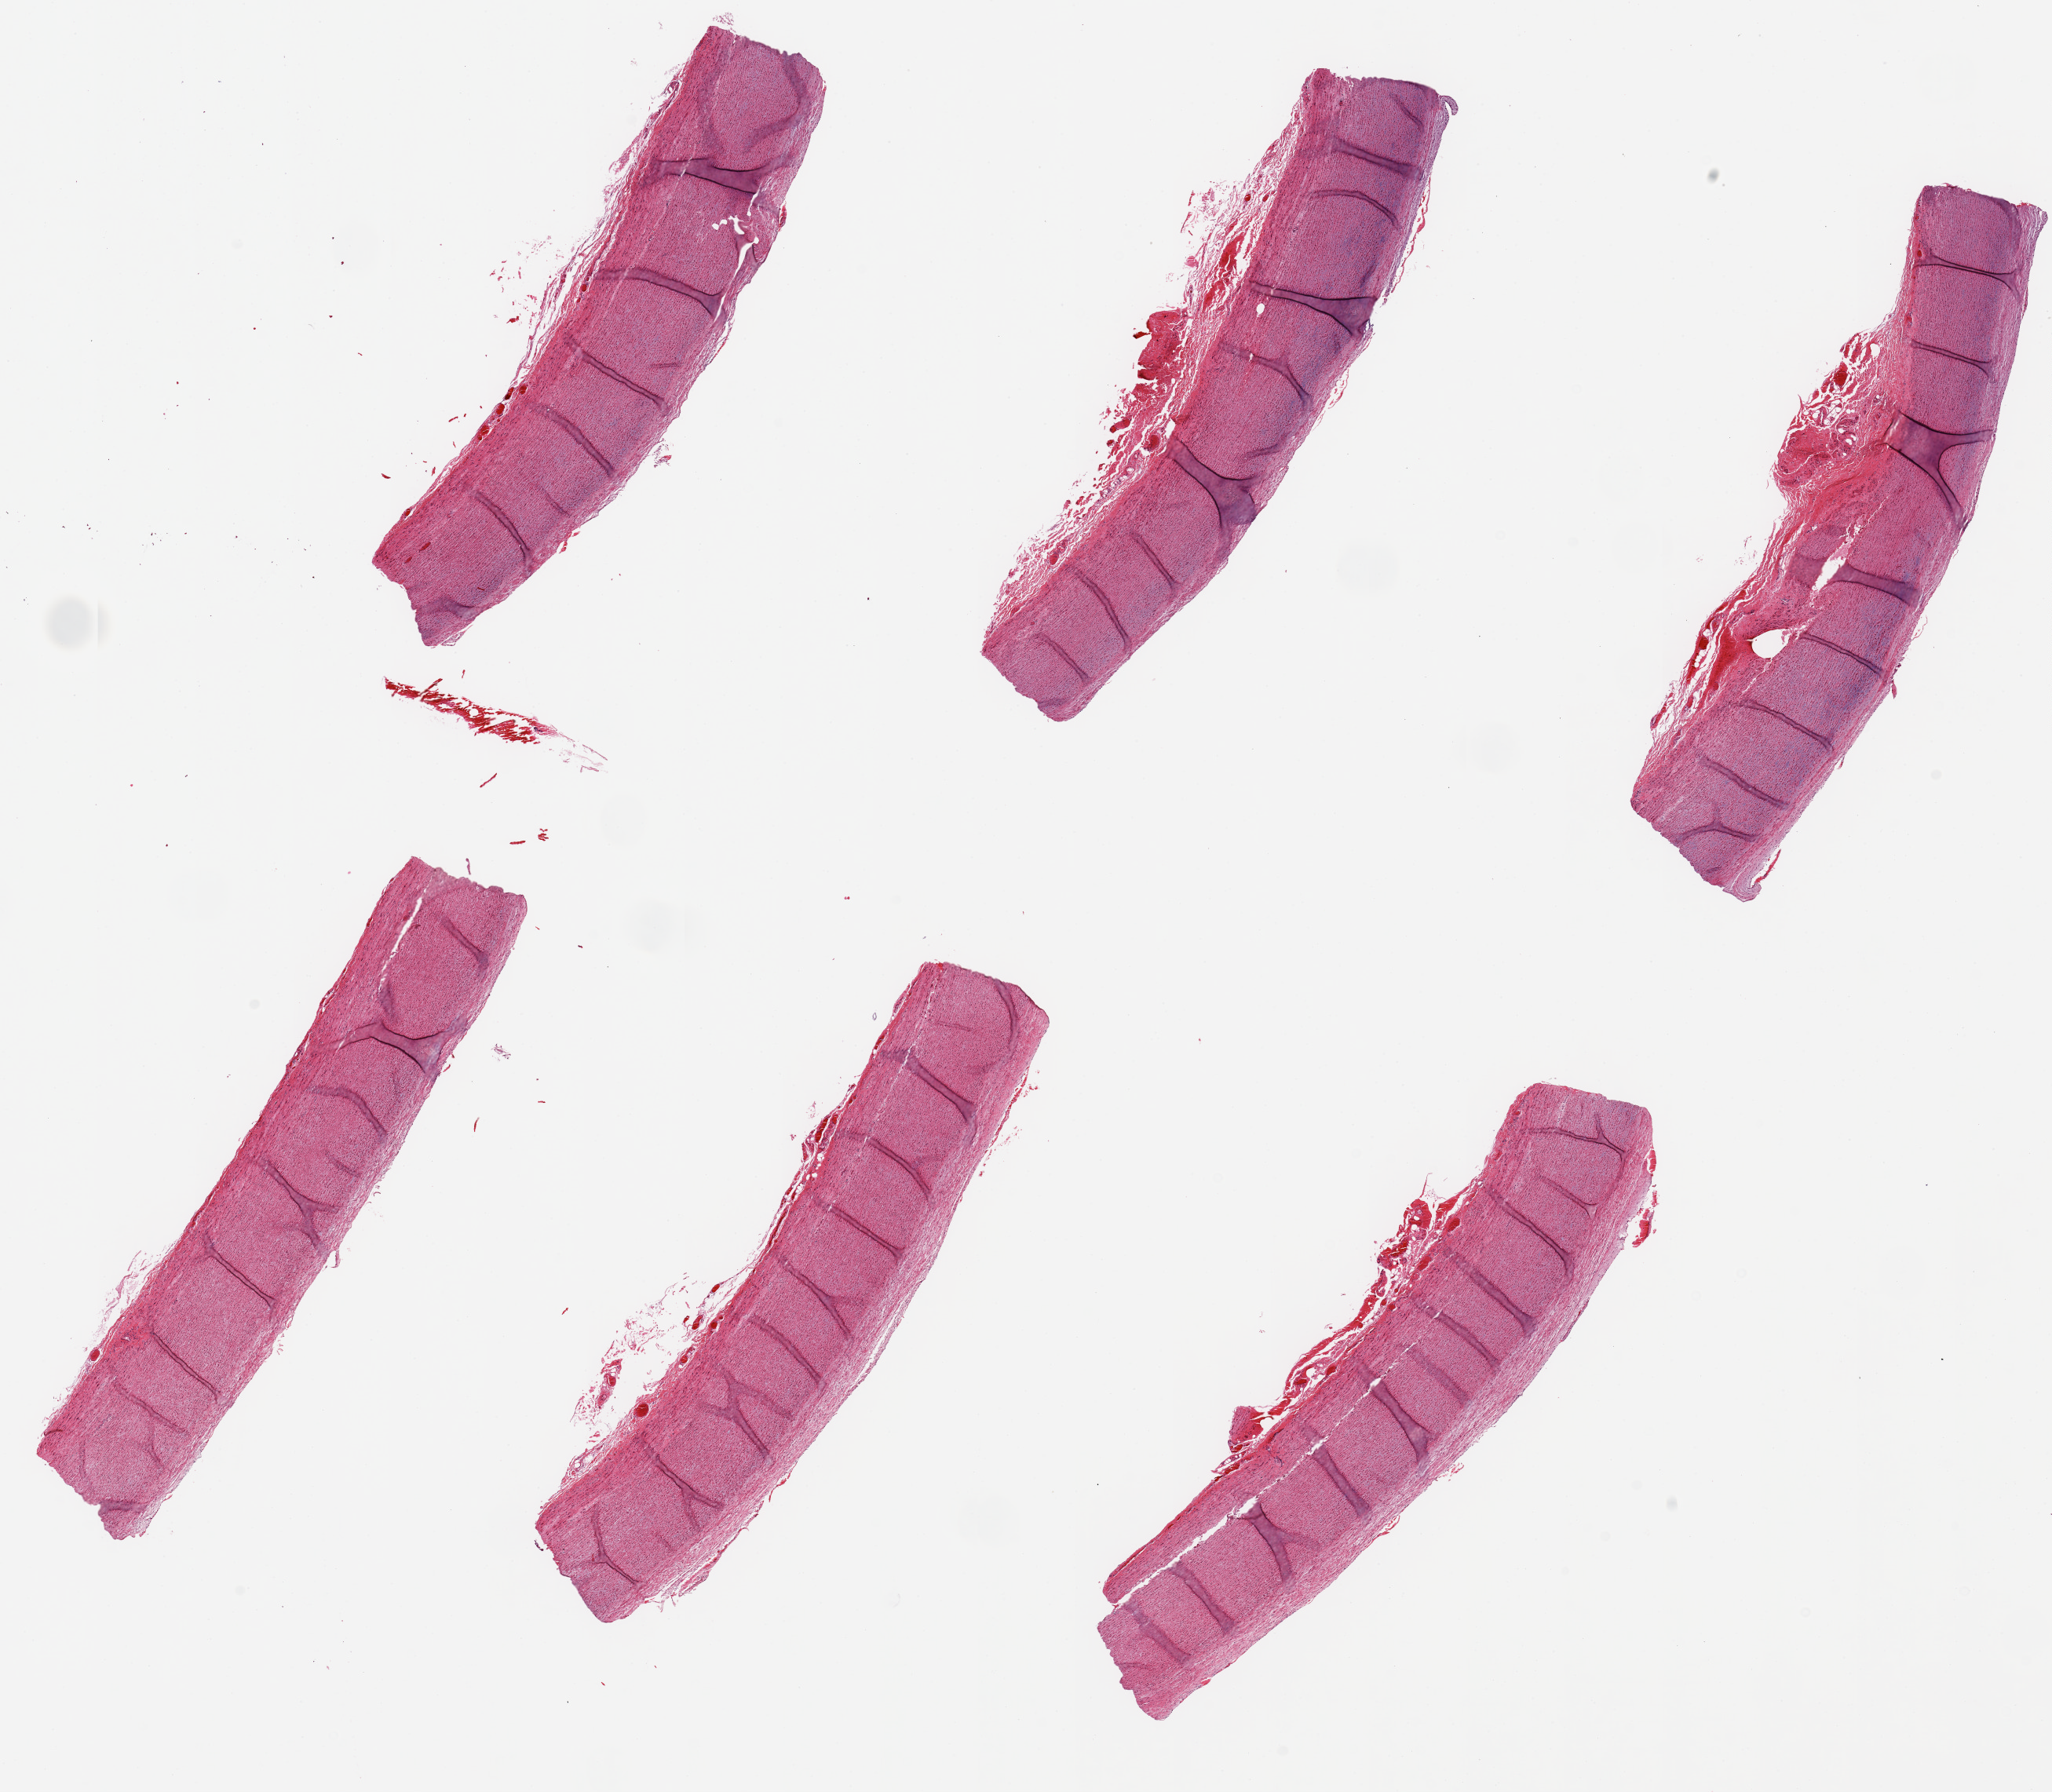
Digitized H&E-stained section — shown as a low-resolution overview of the whole scanned area (about 20.7 x 18.1 mm); PAXgene-fixed, paraffin-embedded tissue; section of aorta (target tissue); donor tissue sample. Donor: male.
• pathologist's review note for this sample: 6 pieces, ~7x1.5mm